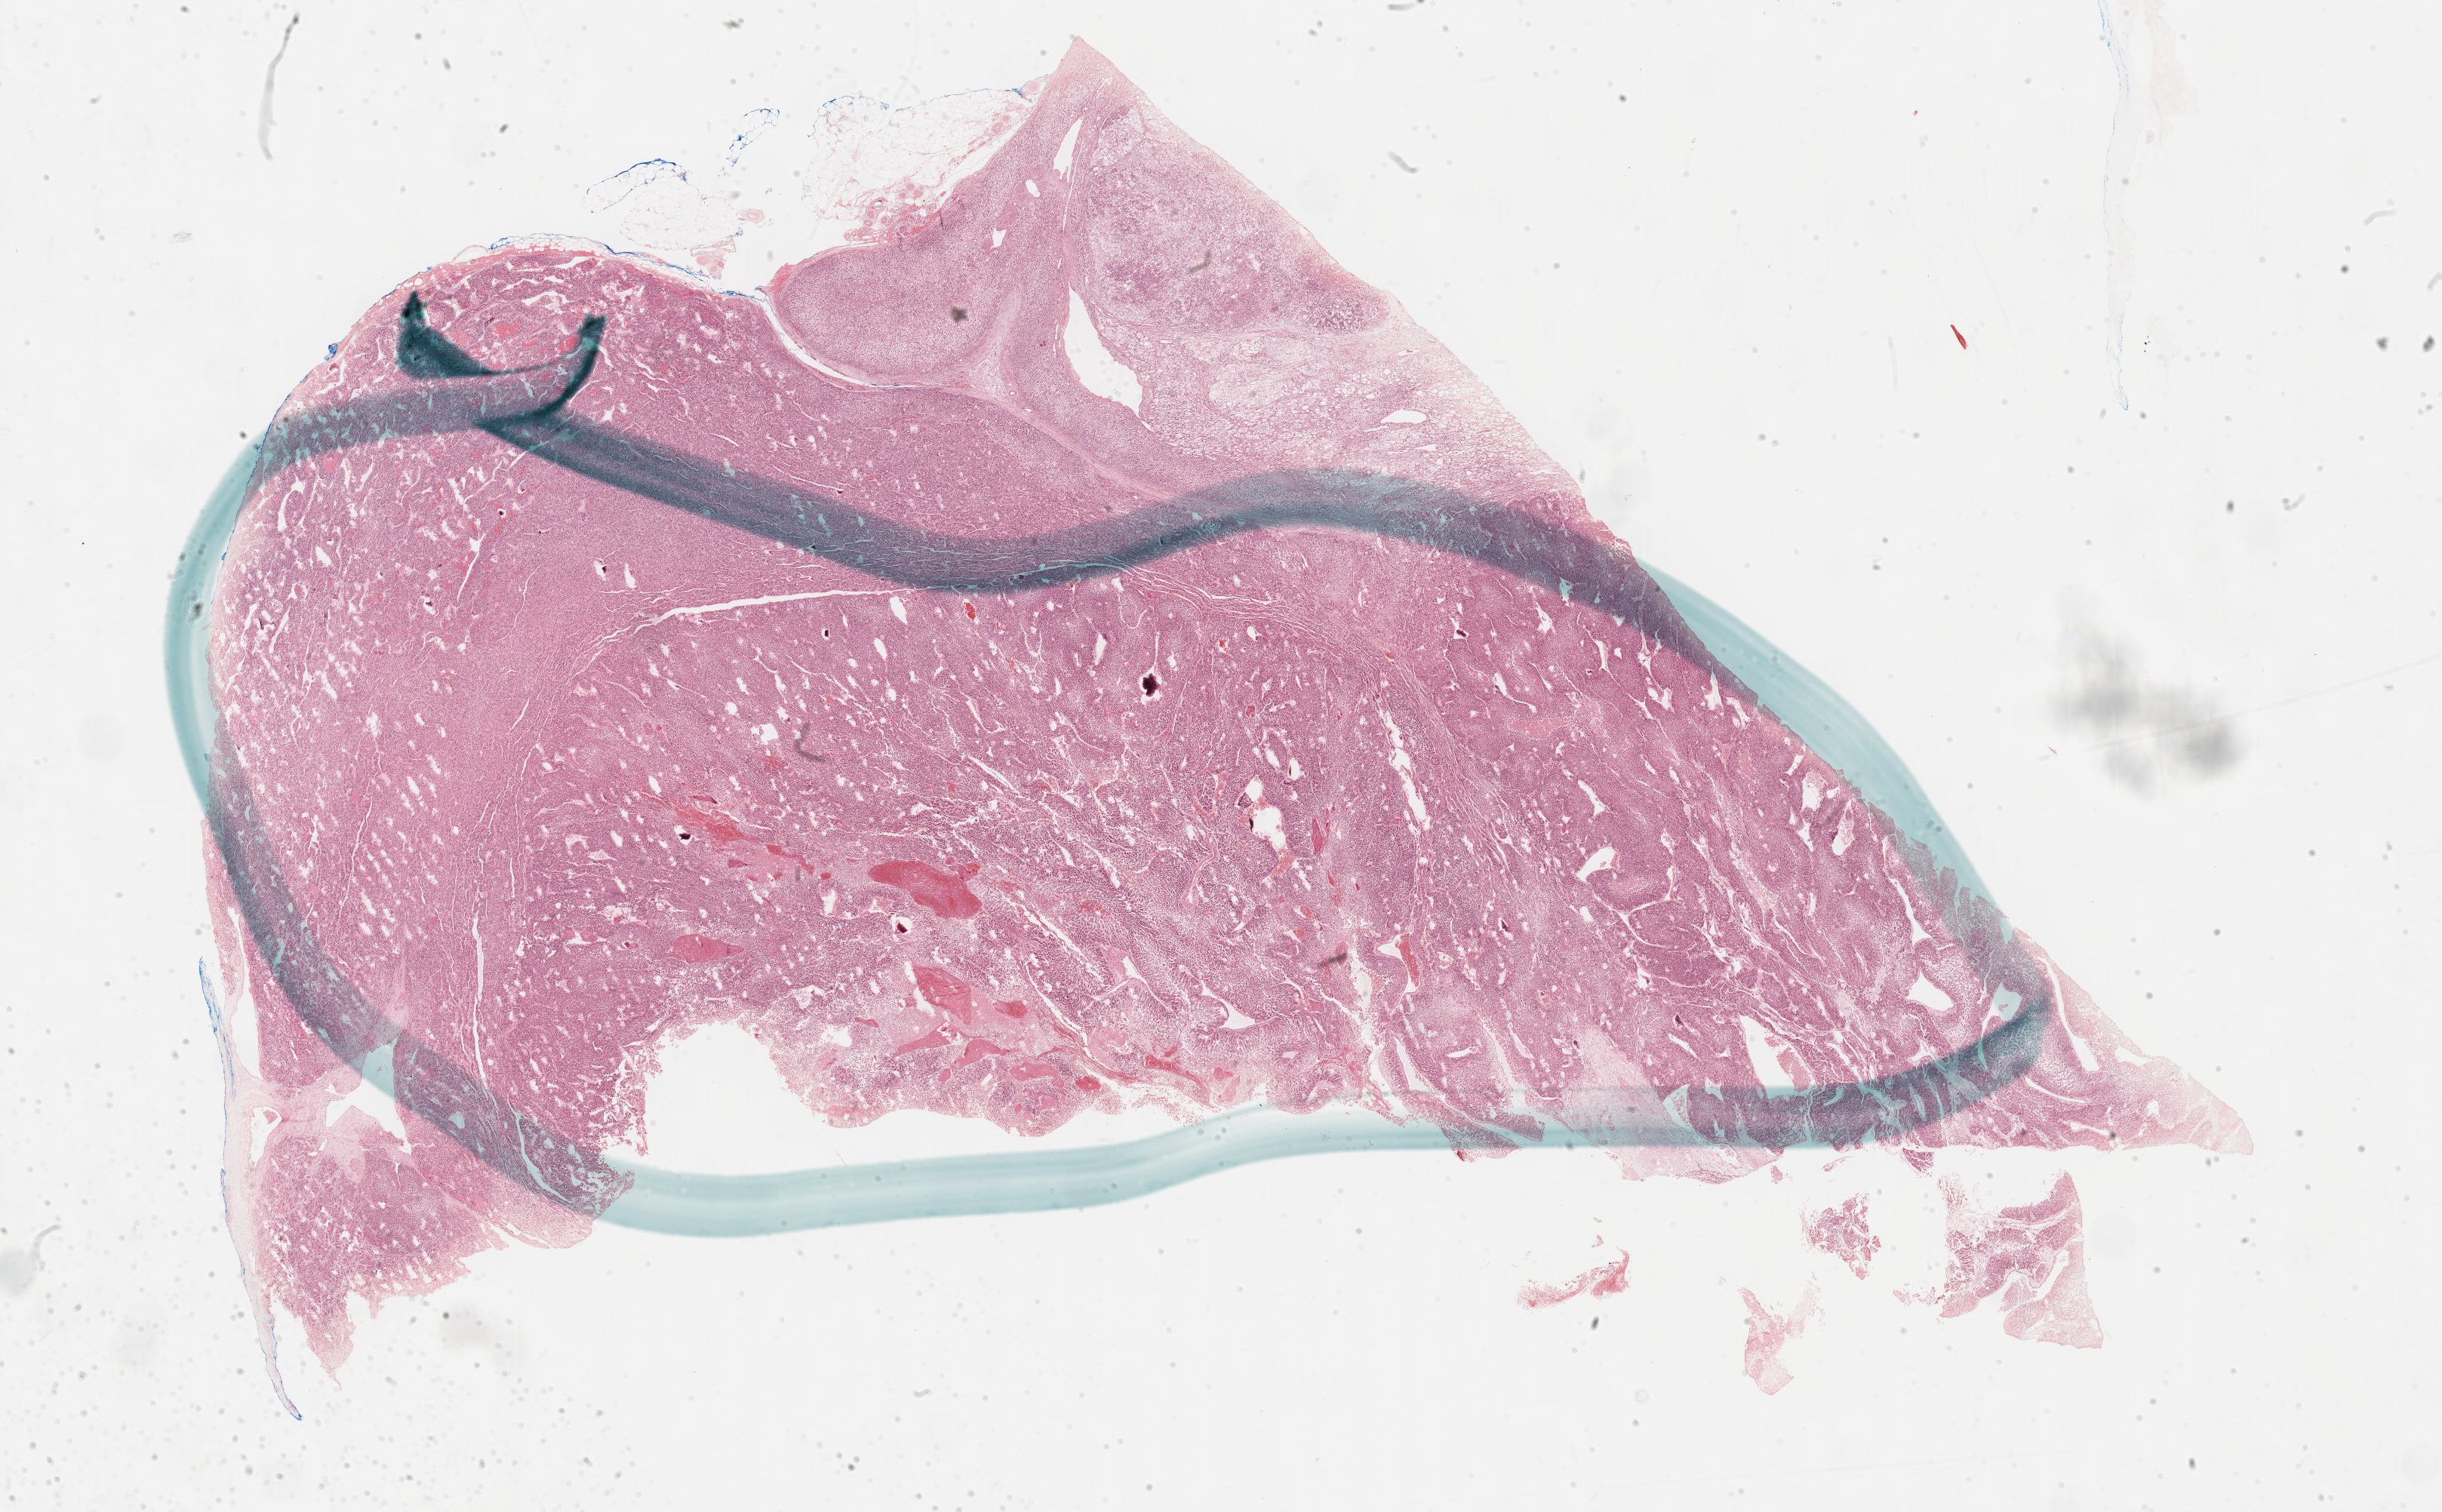
Whole-slide histology image, H&E-stained — whole scanned area (about 26.2 x 16.2 mm) shown as a low-resolution overview; FFPE section; primary tumour sample from the adrenal cortex. Female, age 61 years at initial diagnosis.
Laterality: right. Histologic diagnosis: Adrenal cortical carcinoma (cortex of adrenal gland).